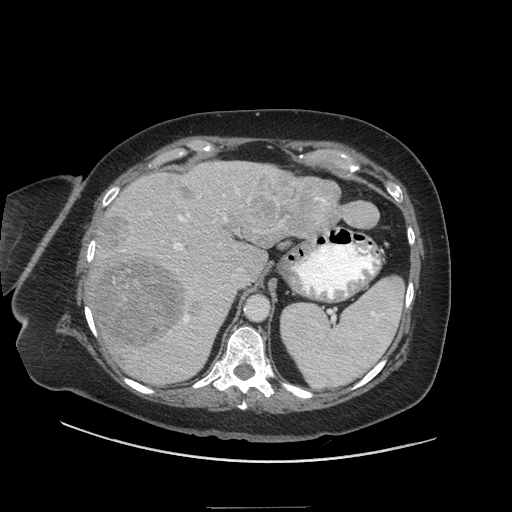
Contrast-enhanced abdominal CT (liver protocol), one axial slice; position 38 of 81 along the scan axis; reconstruction kernel STANDARD; soft-tissue window (W 400 / L 40 HU); 2.5 mm slice thickness; 512 × 512 image matrix, field of view 440 × 440 mm. Case-level facts recorded for this patient, not image findings: diagnosis: hepatocellular carcinoma (patient treated with transarterial chemoembolisation; whether this scan precedes or follows treatment is not stated here); TNM stage (as recorded): Stage-II; Child-Pugh class: A; tumour differentiation: moderately differentiated; tumour nodularity: multinodular.
Outlined on this slice (semi-automatic segmentation, software-assisted and operator-edited):
- liver parenchyma outside the tumour (the mass and vessels are separate outlines, so this box may not span the whole liver): box from (x=88, y=160) to (x=329, y=384) px
- mass: (x=89, y=174)–(x=380, y=347)
- liver vessels: (x=122, y=188)–(x=242, y=324)